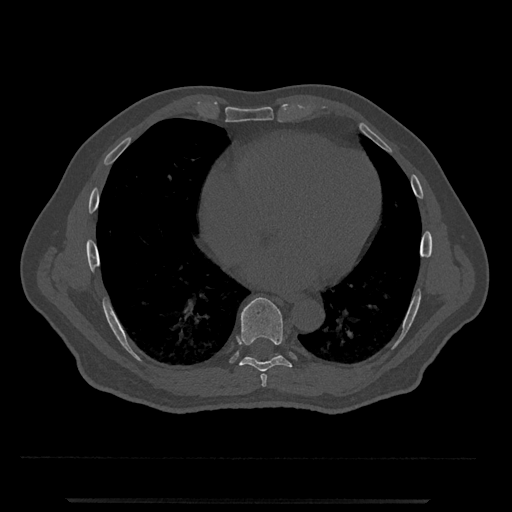
CT including the spine, one axial slice. Position 623 of 797 along the scan axis. 120 kVp. Bone window (W 1800 / L 400 HU). 0.5 mm slice thickness. 512 × 512 image matrix, field of view 419 × 419 mm. Male patient, age 63 years. From the clinical record (not read from this slice): primary cancer: prostate.
Outlined on this slice (semi-automatically segmented with operator editing):
- T7 vertebra: box from (x=260, y=374) to (x=267, y=387) px
- T8 vertebra: (x=239, y=297)–(x=292, y=372)
- T9 vertebra: (x=248, y=353)–(x=278, y=358)